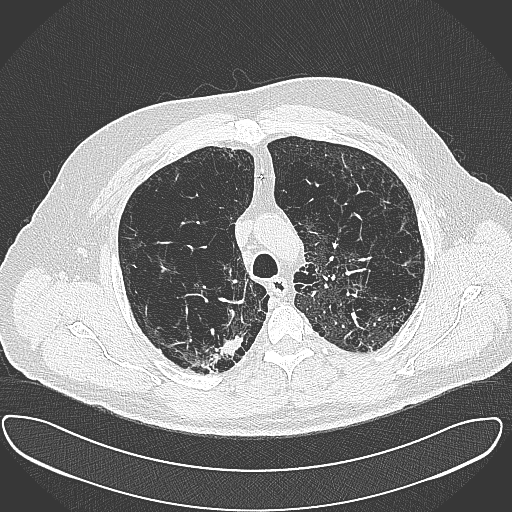
Low-dose screening chest CT, axial slice, first (baseline) screen, lung window (W 1500 / L -600 HU), 1 mm slice thickness, 512 × 512 image matrix, field of view 408 × 408 mm. Male, age 60 years at enrolment. Current smoker at enrolment.
Expert reader's lesion annotation, box from (x=193, y=327) to (x=248, y=376) px. Screening reader's record for this exam (one nodule recorded; not confirmed to be the boxed lesion): non-calcified nodule or mass ≥4 mm, right upper lobe, 15 × 25 mm, spiculated (stellate) margins, soft tissue attenuation. Participant outcome: lung cancer diagnosed 32 days after this screen — carcinoma, NOS, right upper lobe, moderately differentiated (G2), stage IB (AJCC 6th edition), 35 mm at pathology.